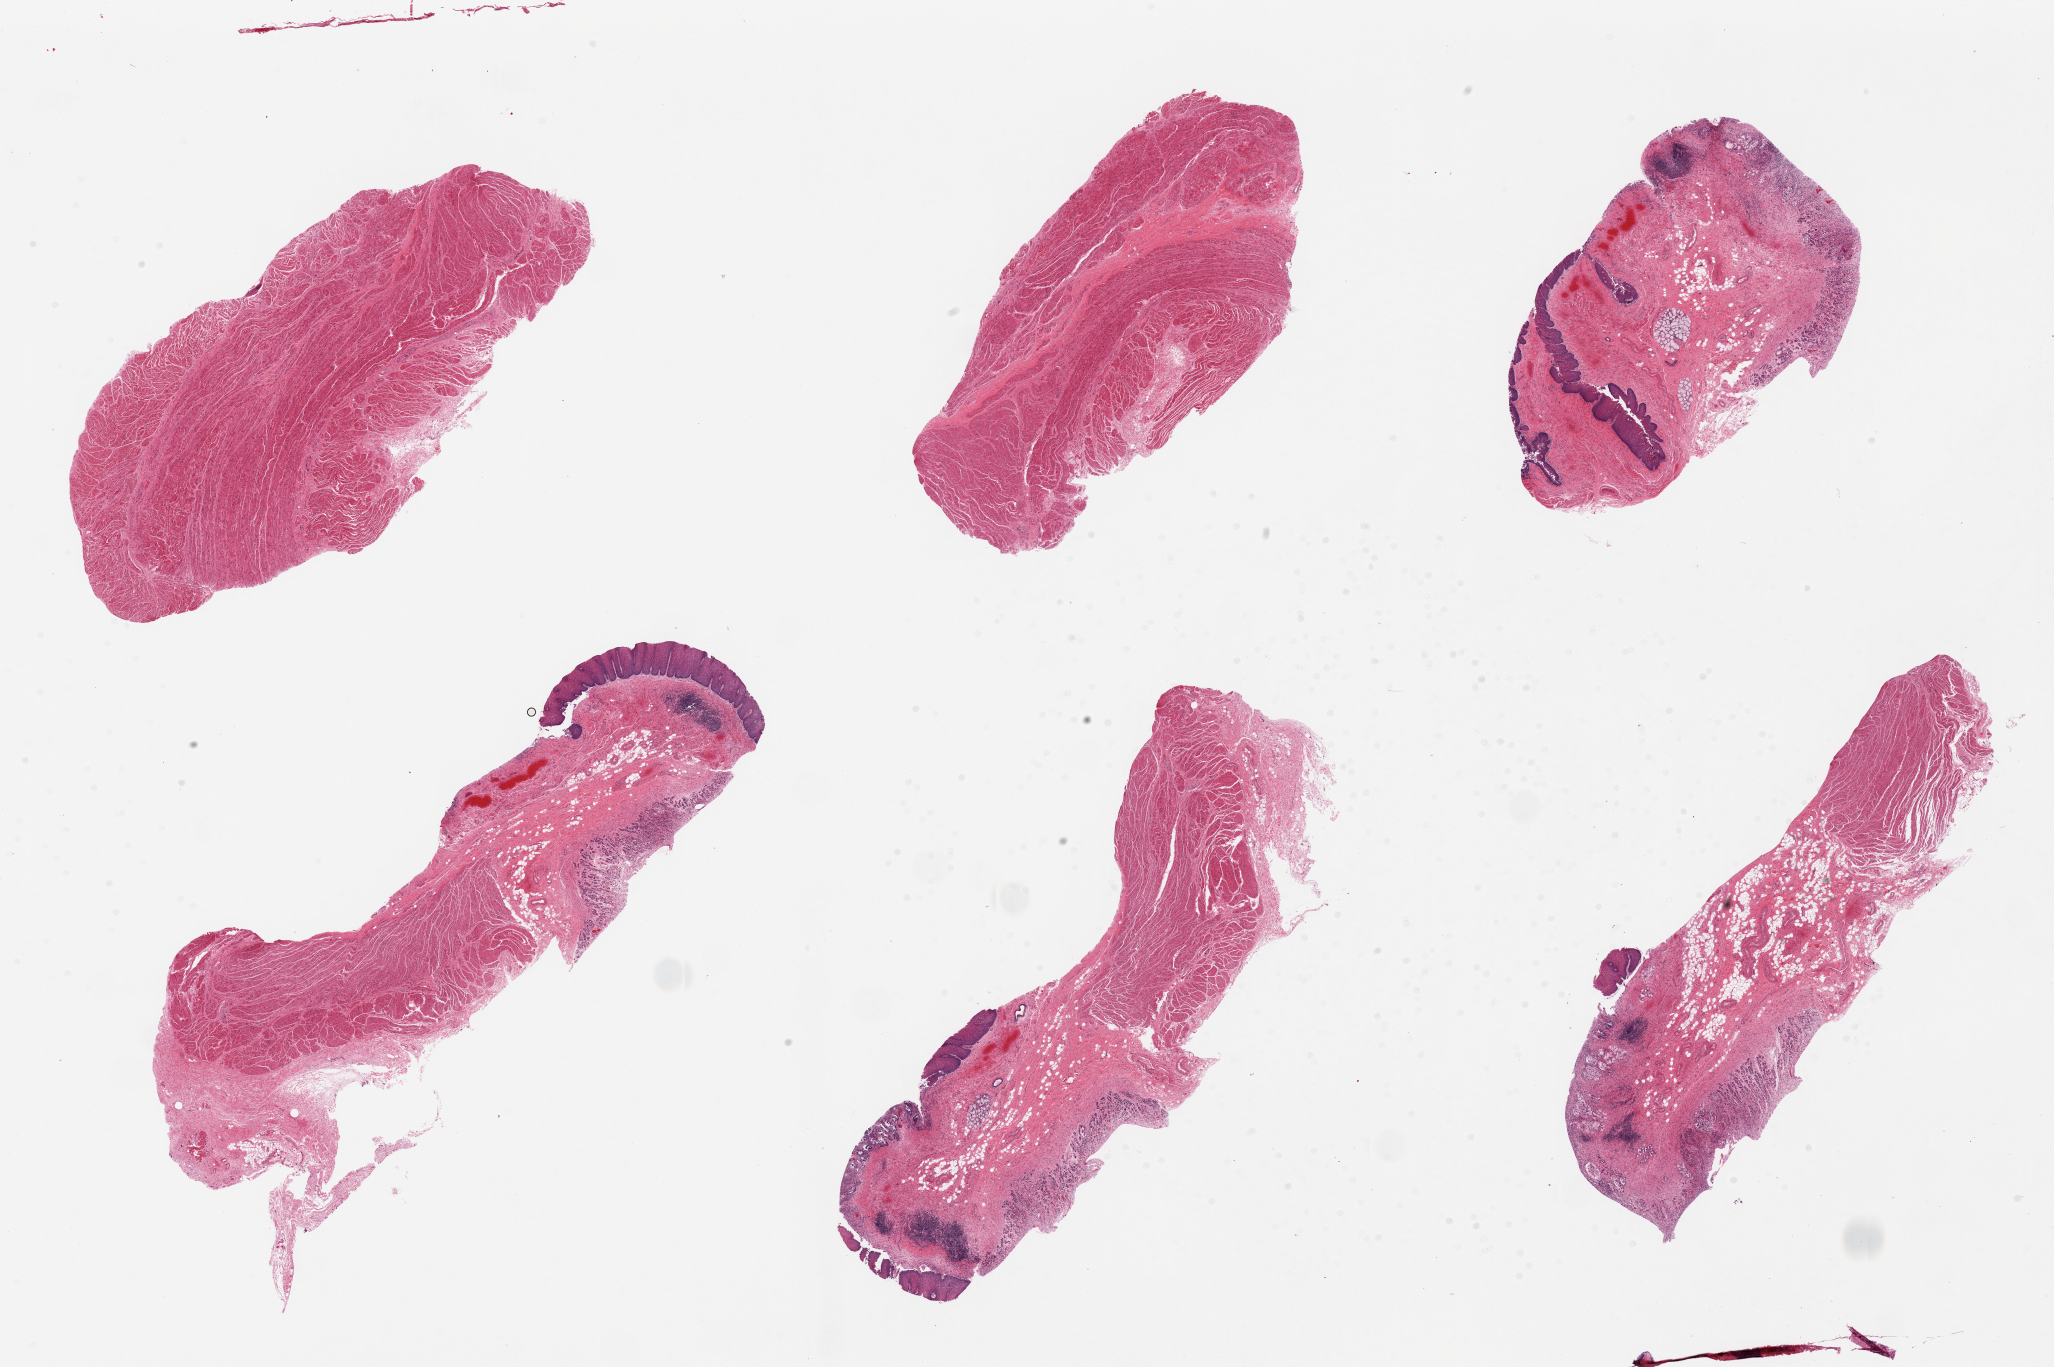
Whole-slide image, haematoxylin and eosin stain, brightfield — whole scanned area (about 32.5 x 21.6 mm) shown as a low-resolution overview. Female donor.
- specimen: PAXgene-fixed, paraffin-embedded tissue; section of gastroesophageal junction (target tissue); tissue donor sample